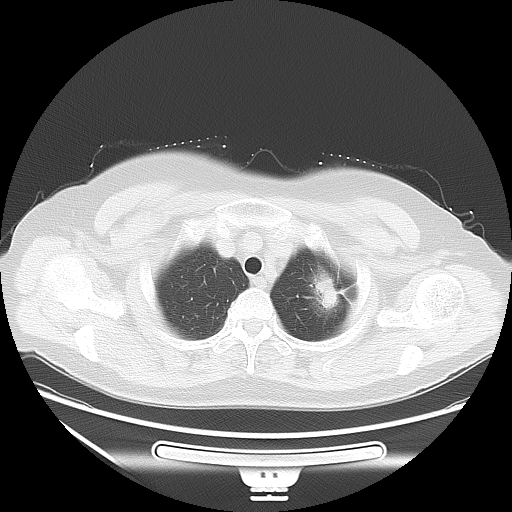
Chest CT, one axial slice; position 48 of 53 along the scan axis; reconstruction kernel LUNG; 120 kVp; lung window (W 1500 / L -600 HU); 512 × 512 image matrix, field of view 403 × 403 mm. Female patient, age 66 years. Case-level facts recorded for this patient, not image findings: clinical TNM (as recorded): T2 N0 M0; histopathological grade: G2.
Outlined on this slice (rectangle marked by the reading radiologist):
- lung tumour (recorded histology: adenocarcinoma): bounding box <298,260,348,320> (left, top, right, bottom; pixels)